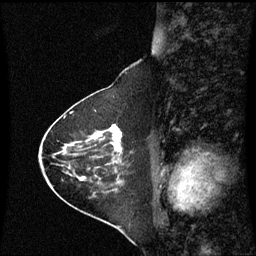
Breast MRI (dynamic contrast-enhanced), one sagittal slice; position 26 of 60 along the scan axis; dynamic contrast-enhanced series, image 2 of 3 at this slice position (ordered by acquisition); 1.5 T; TE 4.2 ms, TR 8.9 ms; 256 × 256 image matrix, field of view 210 × 210 mm. Female patient, age 63 years. Case-level facts recorded for this patient, not image findings: setting: breast cancer imaged before/during neoadjuvant chemotherapy; receptor status: HR-positive, HER2-negative.
Structures marked on this image (semi-automatically segmented with operator editing):
- analysis volume of interest (the breast-tissue region the enhancement analysis was run in; not a lesion): bounding box (x1, y1, x2, y2) in pixels: (88, 125, 124, 163)
- tumour enhancement mask (voxels above the 70 % enhancement threshold inside the analysis volume of interest): (111, 126, 122, 153)